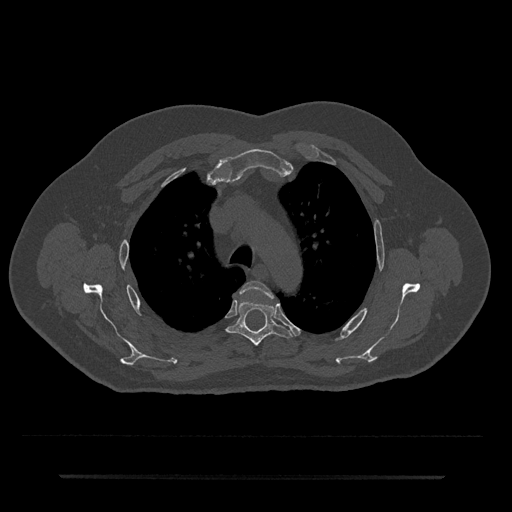
CT including the spine, one axial slice. Position 534 of 797 along the scan axis. 120 kVp. Bone window (W 1800 / L 400 HU). 0.5 mm slice thickness. 512 × 512 image matrix, field of view 437 × 437 mm. Male patient, age 69 years. Case-level facts recorded for this patient, not image findings: primary cancer: prostate.
Annotated regions visible in this slice (semi-automatically segmented with operator editing):
- T3 vertebra: bounding box (x1, y1, x2, y2) in pixels: (241, 281, 274, 298)
- T4 vertebra: (226, 299, 292, 346)